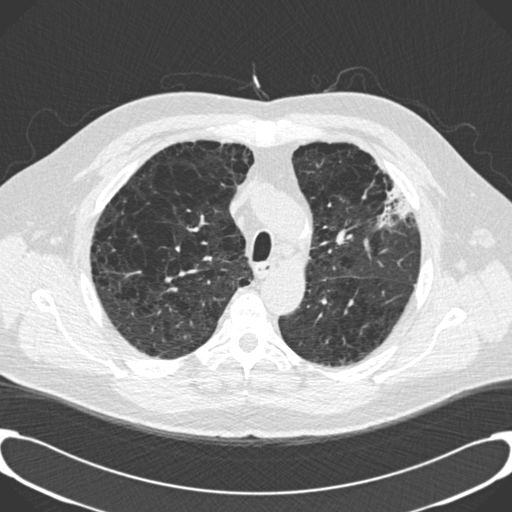
Low-dose screening chest CT, one axial slice; slice 146 of 189 in the series (ordered by position); reconstruction kernel B30f; lung window (W 1500 / L -600 HU); 2 mm slice thickness; 512 × 512 image matrix.
Structures marked on this image (outlined manually by an expert reader):
- lesion 1 (tumor, upper lobe of left lung): bounding box [x1, y1, x2, y2] px = [378, 184, 412, 228]